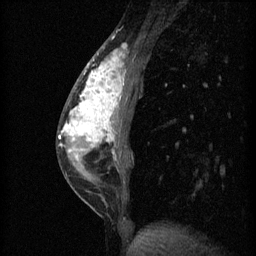
Breast MRI (dynamic contrast-enhanced), one sagittal slice; position 21 of 60 along the scan axis; 3 images stored at this slice position (order not interpretable as contrast timing); 1.5 T; TE 4.2 ms, TR 11 ms; 2 mm slice thickness; 256 × 256 image matrix, field of view 180 × 180 mm. Female patient, age 40 years.
Outlined on this slice (semi-automatically segmented with operator editing):
- analysis volume of interest (the breast-tissue region the enhancement analysis was run in; not a lesion): bounding box <58,42,141,203> (left, top, right, bottom; pixels)
- tumour enhancement mask (voxels above the 70 % enhancement threshold inside the analysis volume of interest): <60,50,125,159>